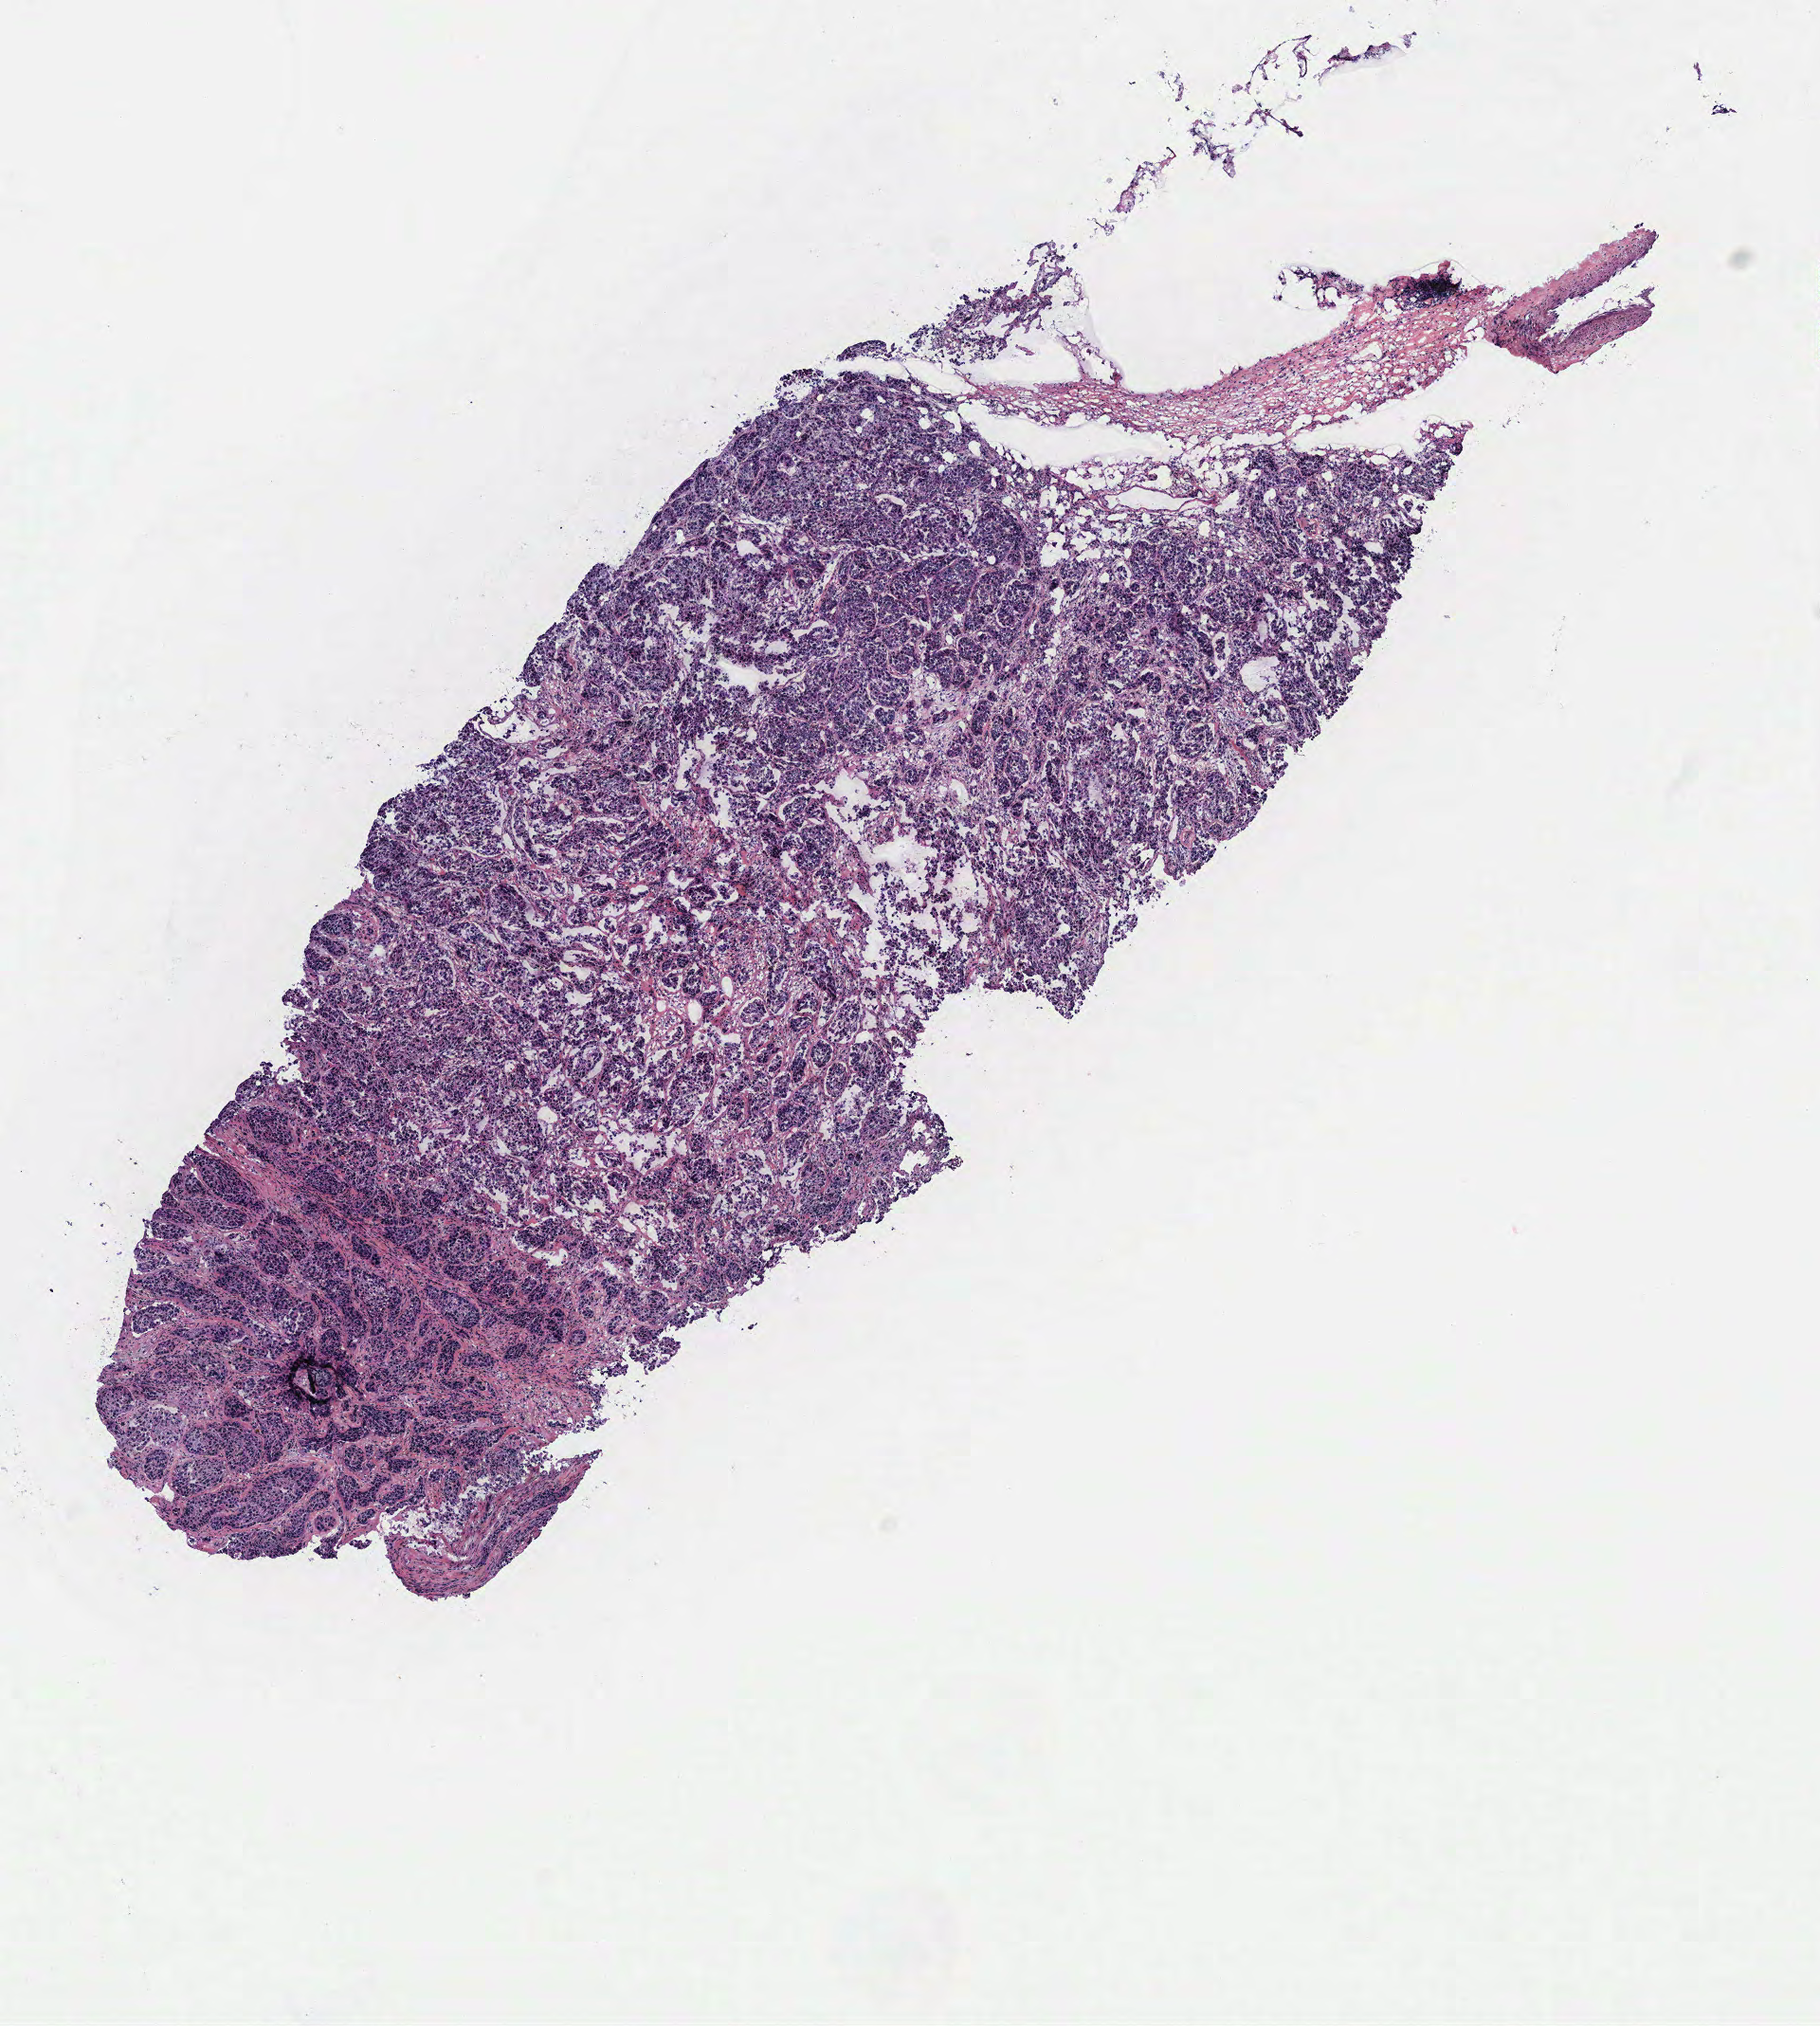
Whole-slide histology image, Hematoxylin and eosin (H&E) stained — low-resolution overview of the scanned area, about 7.7 x 8.6 mm. Tumour tissue sample, breast. 55-year-old female patient.
AJCC pathologic stage: IIB. Histologic diagnosis: Infiltrating duct carcinoma, NOS.